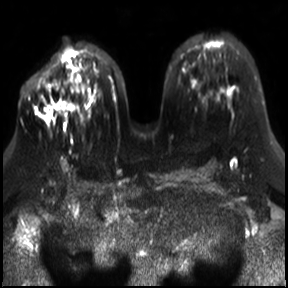
Breast MRI, one axial slice. Slice 17 of 30 in the series (ordered by position). Diffusion-weighted series; image 2 of 4 stored at this slice position (different b-values; order by instance number). 3 T. 288 × 288 image matrix. Female patient.
Structures marked on this image (manually delineated by an expert):
- tumour on diffusion-weighted imaging: bounding box <42,105,60,121> (left, top, right, bottom; pixels)